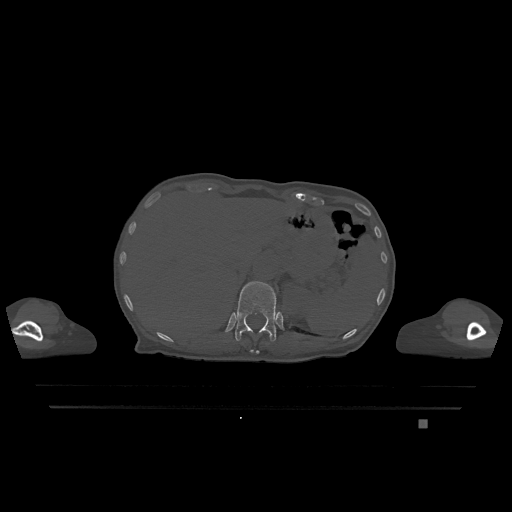
CT including the spine, one axial slice; position 545 of 1317 along the scan axis; bone window (W 1800 / L 400 HU); 512 × 512 image matrix, field of view 500 × 500 mm. Female patient, age 74 years. From the clinical record (not read from this slice): primary cancer: lung.
Outlined on this slice (semi-automatically segmented with operator editing):
- T11 vertebra: box from (x=250, y=350) to (x=260, y=354) px
- T12 vertebra: (x=235, y=281)–(x=276, y=342)